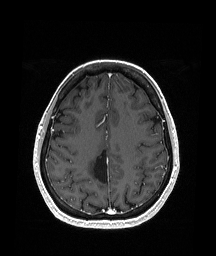
Brain MRI from a brain-tumour surgery series, one axial slice. Slice 66 of 151 in the series (ordered by position). T1-weighted post-contrast. 1.05 mm slice thickness. 216 × 256 image matrix, field of view 211 × 250 mm. From the clinical record (not read from this slice): histopathology: Oligodendroglioma; WHO grade: 2; IDH mutation: yes; tumour location: Right Parietal.
Annotated regions visible in this slice (expert manual segmentation):
- previous resection cavity: bounding box [x1, y1, x2, y2] px = [94, 149, 109, 183]